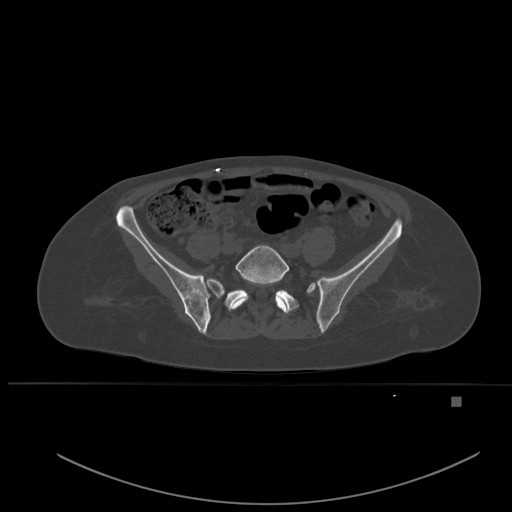
CT including the spine, one axial slice. Position 147 of 651 along the scan axis. Bone window (W 1800 / L 400 HU). 512 × 512 image matrix, field of view 443 × 443 mm. Female patient, age 49 years. Case-level facts recorded for this patient, not image findings: primary cancer: breast.
Outlined on this slice (semi-automatic segmentation, software-assisted and operator-edited):
- L5 vertebra: bounding box <230,245,290,314> (left, top, right, bottom; pixels)